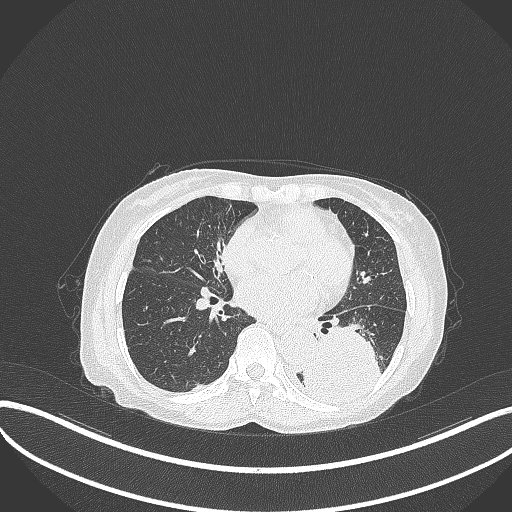
Chest CT, one axial slice; position 137 of 370 along the scan axis; 120 kVp; lung window (W 1500 / L -600 HU); 1 mm slice thickness; 512 × 512 image matrix, field of view 400 × 400 mm. Patient: female, 78 years. Case-level facts recorded for this patient, not image findings: clinical TNM (as recorded): T3 N0 M1.
Outlined on this slice (rectangle marked by the reading radiologist):
- lung tumour (recorded histology: squamous cell carcinoma): box from (x=292, y=324) to (x=383, y=403) px